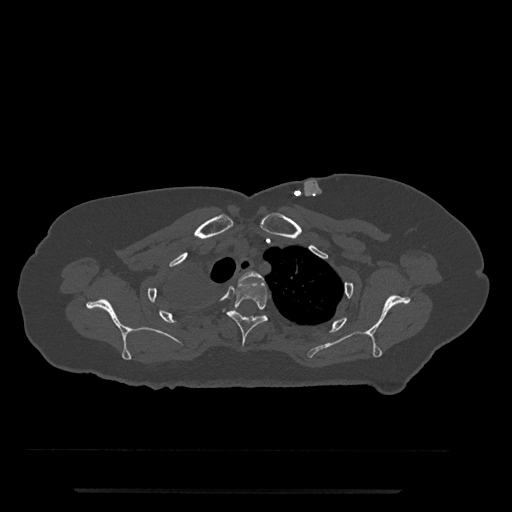
CT including the spine, one axial slice; slice 632 of 797 in the series (ordered by position); reconstruction kernel Br40s/3; 120 kVp; bone window (W 1800 / L 400 HU); 0.5 mm slice thickness; 512 × 512 image matrix, field of view 440 × 440 mm. Patient: female, 51 years. Case-level facts recorded for this patient, not image findings: primary cancer: neuro; vertebrae with lytic lesions (as recorded): T8.
Annotated regions visible in this slice (semi-automatically segmented with operator editing):
- T2 vertebra: bounding box [x1, y1, x2, y2] px = [239, 271, 263, 281]
- T3 vertebra: [216, 280, 268, 347]
- T4 vertebra: [234, 310, 263, 317]